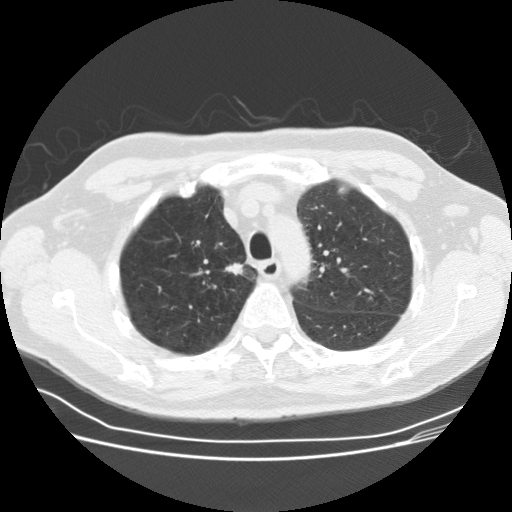
Chest CT (low-dose screening protocol), one axial image; third annual screen; lung window (W 1500 / L -600 HU); 2.5 mm slice thickness; slice 124 of 164 in the series. Male participant, aged 69 years at enrolment.
- Expert-annotated lung lesion, bounding box (x1, y1, x2, y2) in pixels: (220, 256, 257, 289).
- Screening reader's record for this exam (one nodule recorded; not confirmed to be the boxed lesion): non-calcified nodule or mass ≥4 mm, right upper lobe, 12 × 10 mm, spiculated (stellate) margins, soft tissue attenuation, pre-existing on the prior screen: yes; interval growth: yes.
- Official screen result: positive, other.
- Later outcome: lung cancer diagnosed 36 days after this screen — squamous cell carcinoma, NOS, right upper lobe, moderately differentiated (G2), stage IA (AJCC 6th edition), 9 mm at pathology.